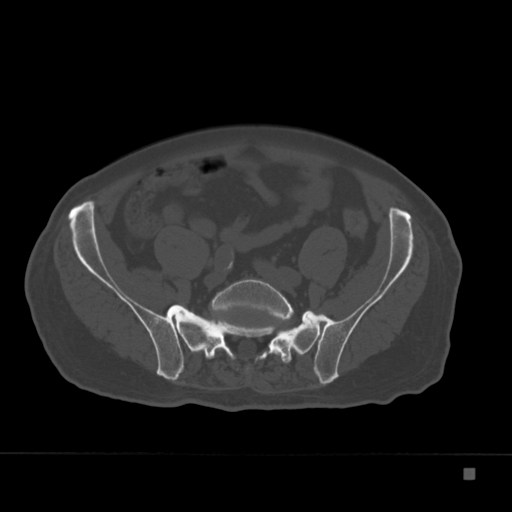
CT including the spine, one axial slice; slice 12 of 332 in the series (ordered by position); 120 kVp; bone window (W 1800 / L 400 HU); 512 × 512 image matrix, field of view 389 × 389 mm. Male patient, age 72 years. Case-level facts recorded for this patient, not image findings: primary cancer: skeletal.
Annotated regions visible in this slice (semi-automatic segmentation, software-assisted and operator-edited):
- L5 vertebra: bounding box <209,279,293,359> (left, top, right, bottom; pixels)